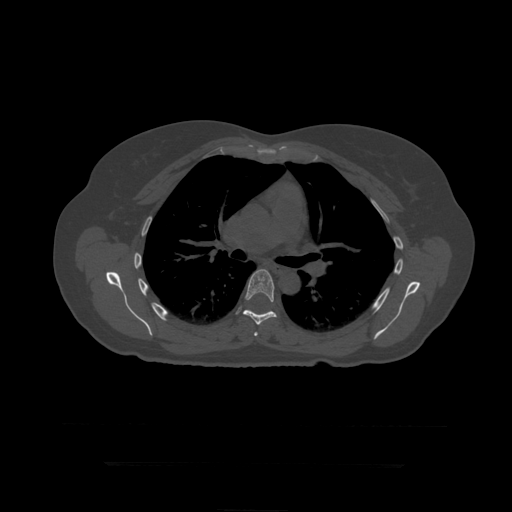
CT including the spine, one axial slice. Reconstruction kernel STANDARD. 120 kVp. Bone window (W 1800 / L 400 HU). 1.25 mm slice thickness. 512 × 512 image matrix, field of view 450 × 450 mm. Patient age 41 years. Case-level facts recorded for this patient, not image findings: primary cancer: breast.
Structures marked on this image (semi-automatic segmentation, software-assisted and operator-edited):
- T6 vertebra: bounding box [x1, y1, x2, y2] px = [254, 332, 258, 336]
- T7 vertebra: [243, 270, 277, 325]